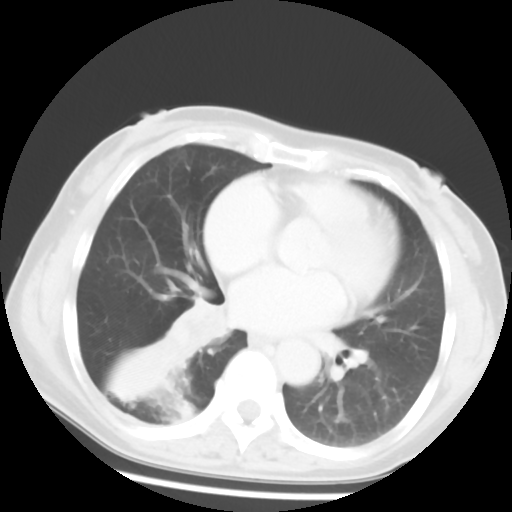
Chest CT, one axial slice. Slice 25 of 52 in the series (ordered by position). 120 kVp. Lung window (W 1500 / L -600 HU). 512 × 512 image matrix, field of view 297 × 297 mm. Female patient, age 54 years. Case-level facts recorded for this patient, not image findings: clinical TNM (as recorded): T1c N0 M0; histopathological grade: G1-2.
Outlined on this slice (rectangle marked by the reading radiologist):
- lung tumour (recorded histology: squamous cell carcinoma): bounding box <166,293,234,368> (left, top, right, bottom; pixels)